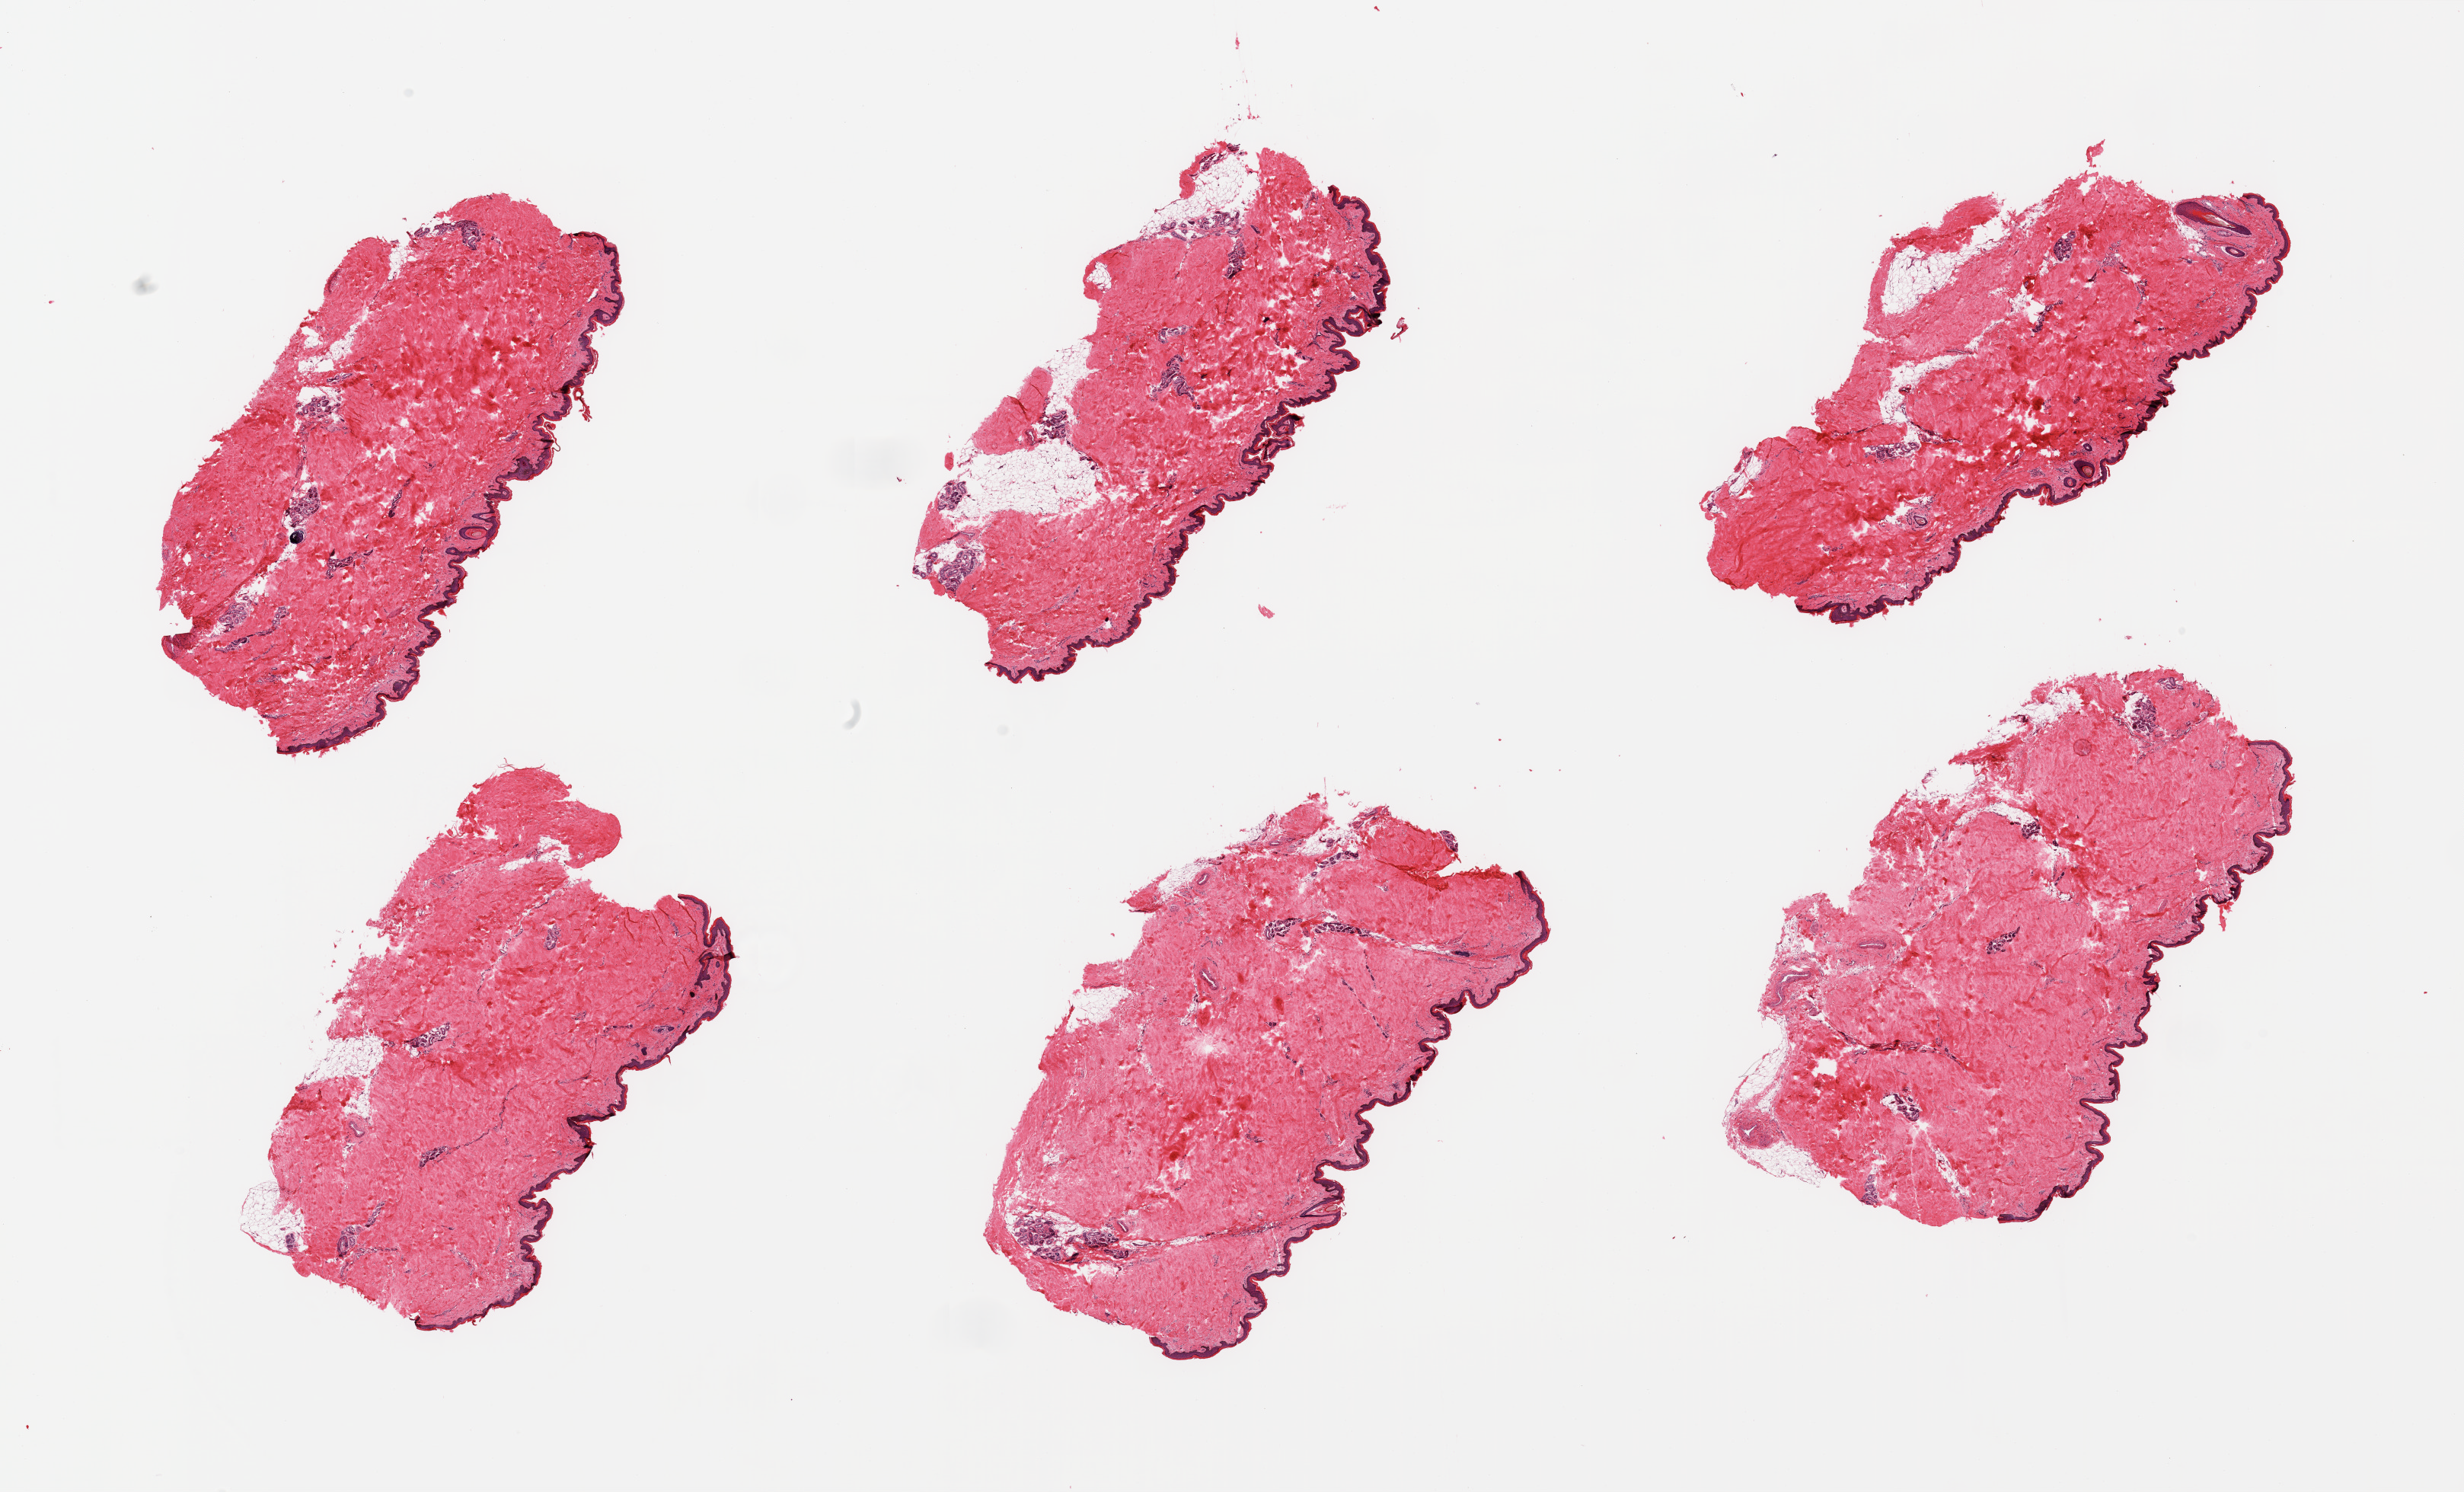
Digitized H&E-stained section, brightfield, a low-resolution overview of the entire scanned area, about 25.6 x 15.5 mm (acquisition: 20x scan); PAXgene-fixed paraffin-embedded (PFPE) section; target tissue: skin of lower leg; donor tissue sample. Male donor.
• reviewer comment on this tissue sample: 6 pieces; epidermis measures 36 microns, few pieces include attached fat up to 15%